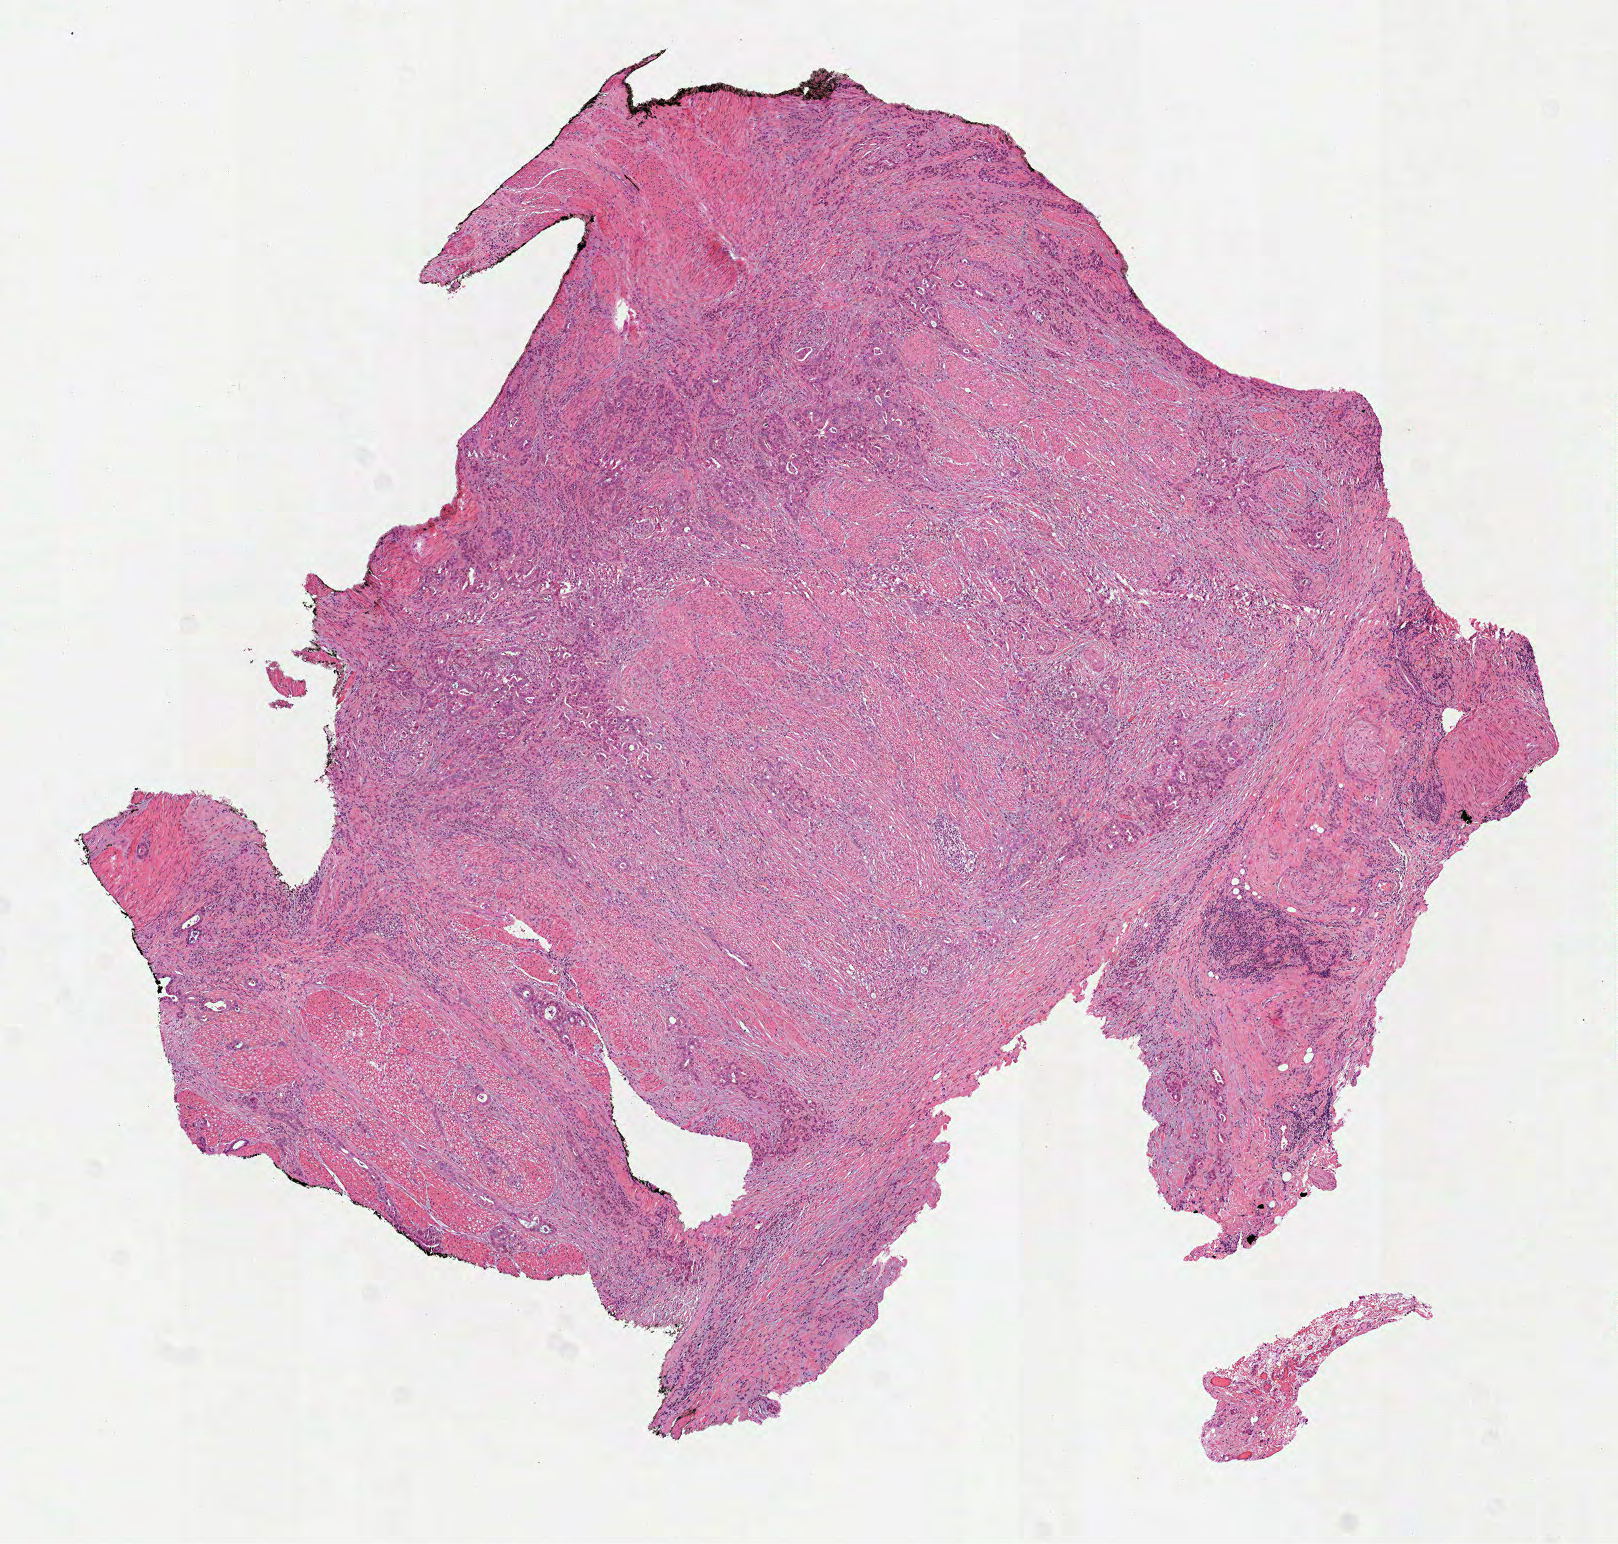
Hematoxylin and eosin (H&E) stained whole-slide image, low-resolution overview of the scanned area, about 6.5 x 6.2 mm (acquisition: 40x scan); formalin-fixed paraffin-embedded (FFPE) diagnostic section; stomach, primary tumour sample. Patient: male, age at initial diagnosis 79 years.
Diagnosis: Adenocarcinoma, NOS (cardia, NOS).